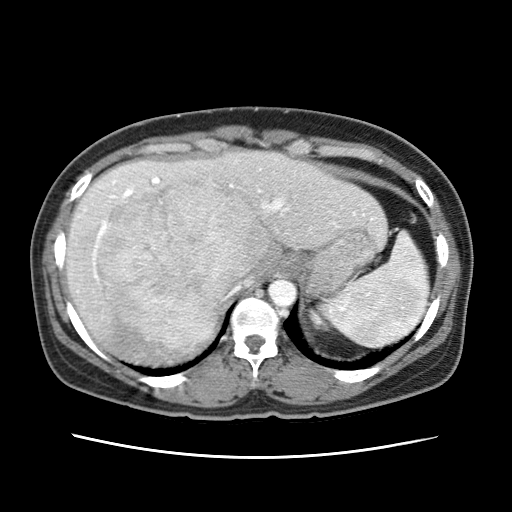
Contrast-enhanced abdominal CT (liver protocol), one axial slice; position 50 of 79 along the scan axis; reconstruction kernel STANDARD; 120 kVp; soft-tissue window (W 400 / L 40 HU); 2.5 mm slice thickness; 512 × 512 image matrix, field of view 340 × 340 mm. From the clinical record (not read from this slice): diagnosis: hepatocellular carcinoma (patient treated with transarterial chemoembolisation; whether this scan precedes or follows treatment is not stated here); TNM stage (as recorded): Stage-I; Child-Pugh class: A; tumour differentiation: moderately differentiated.
Outlined on this slice (semi-automatically segmented with operator editing):
- abdominal aorta: bounding box <268,279,297,306> (left, top, right, bottom; pixels)
- liver parenchyma outside the tumour (the mass and vessels are separate outlines, so this box may not span the whole liver): <64,150,384,364>
- mass: <98,178,269,346>
- liver vessels: <84,177,373,279>